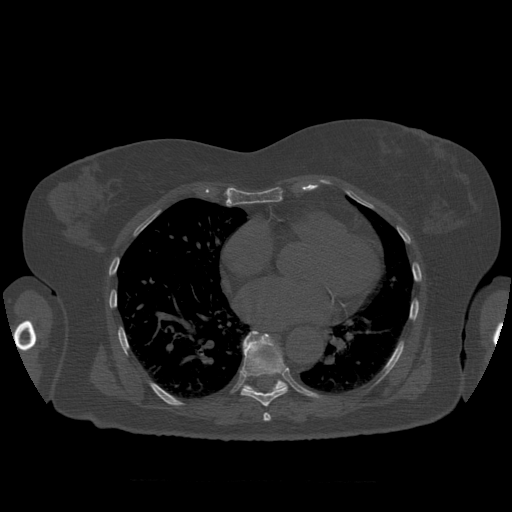
CT including the spine, one axial slice. Position 373 of 399 along the scan axis. Reconstruction kernel STANDARD. 120 kVp. Bone window (W 1800 / L 400 HU). 1.25 mm slice thickness. 512 × 512 image matrix, field of view 404 × 404 mm. Patient age 81 years. Case-level facts recorded for this patient, not image findings: primary cancer: renal; vertebrae with lytic lesions (as recorded): L1.
Structures marked on this image (semi-automatically segmented with operator editing):
- T7 vertebra: bounding box [x1, y1, x2, y2] px = [263, 413, 271, 421]
- T8 vertebra: [241, 331, 288, 407]
- T9 vertebra: [244, 332, 287, 392]